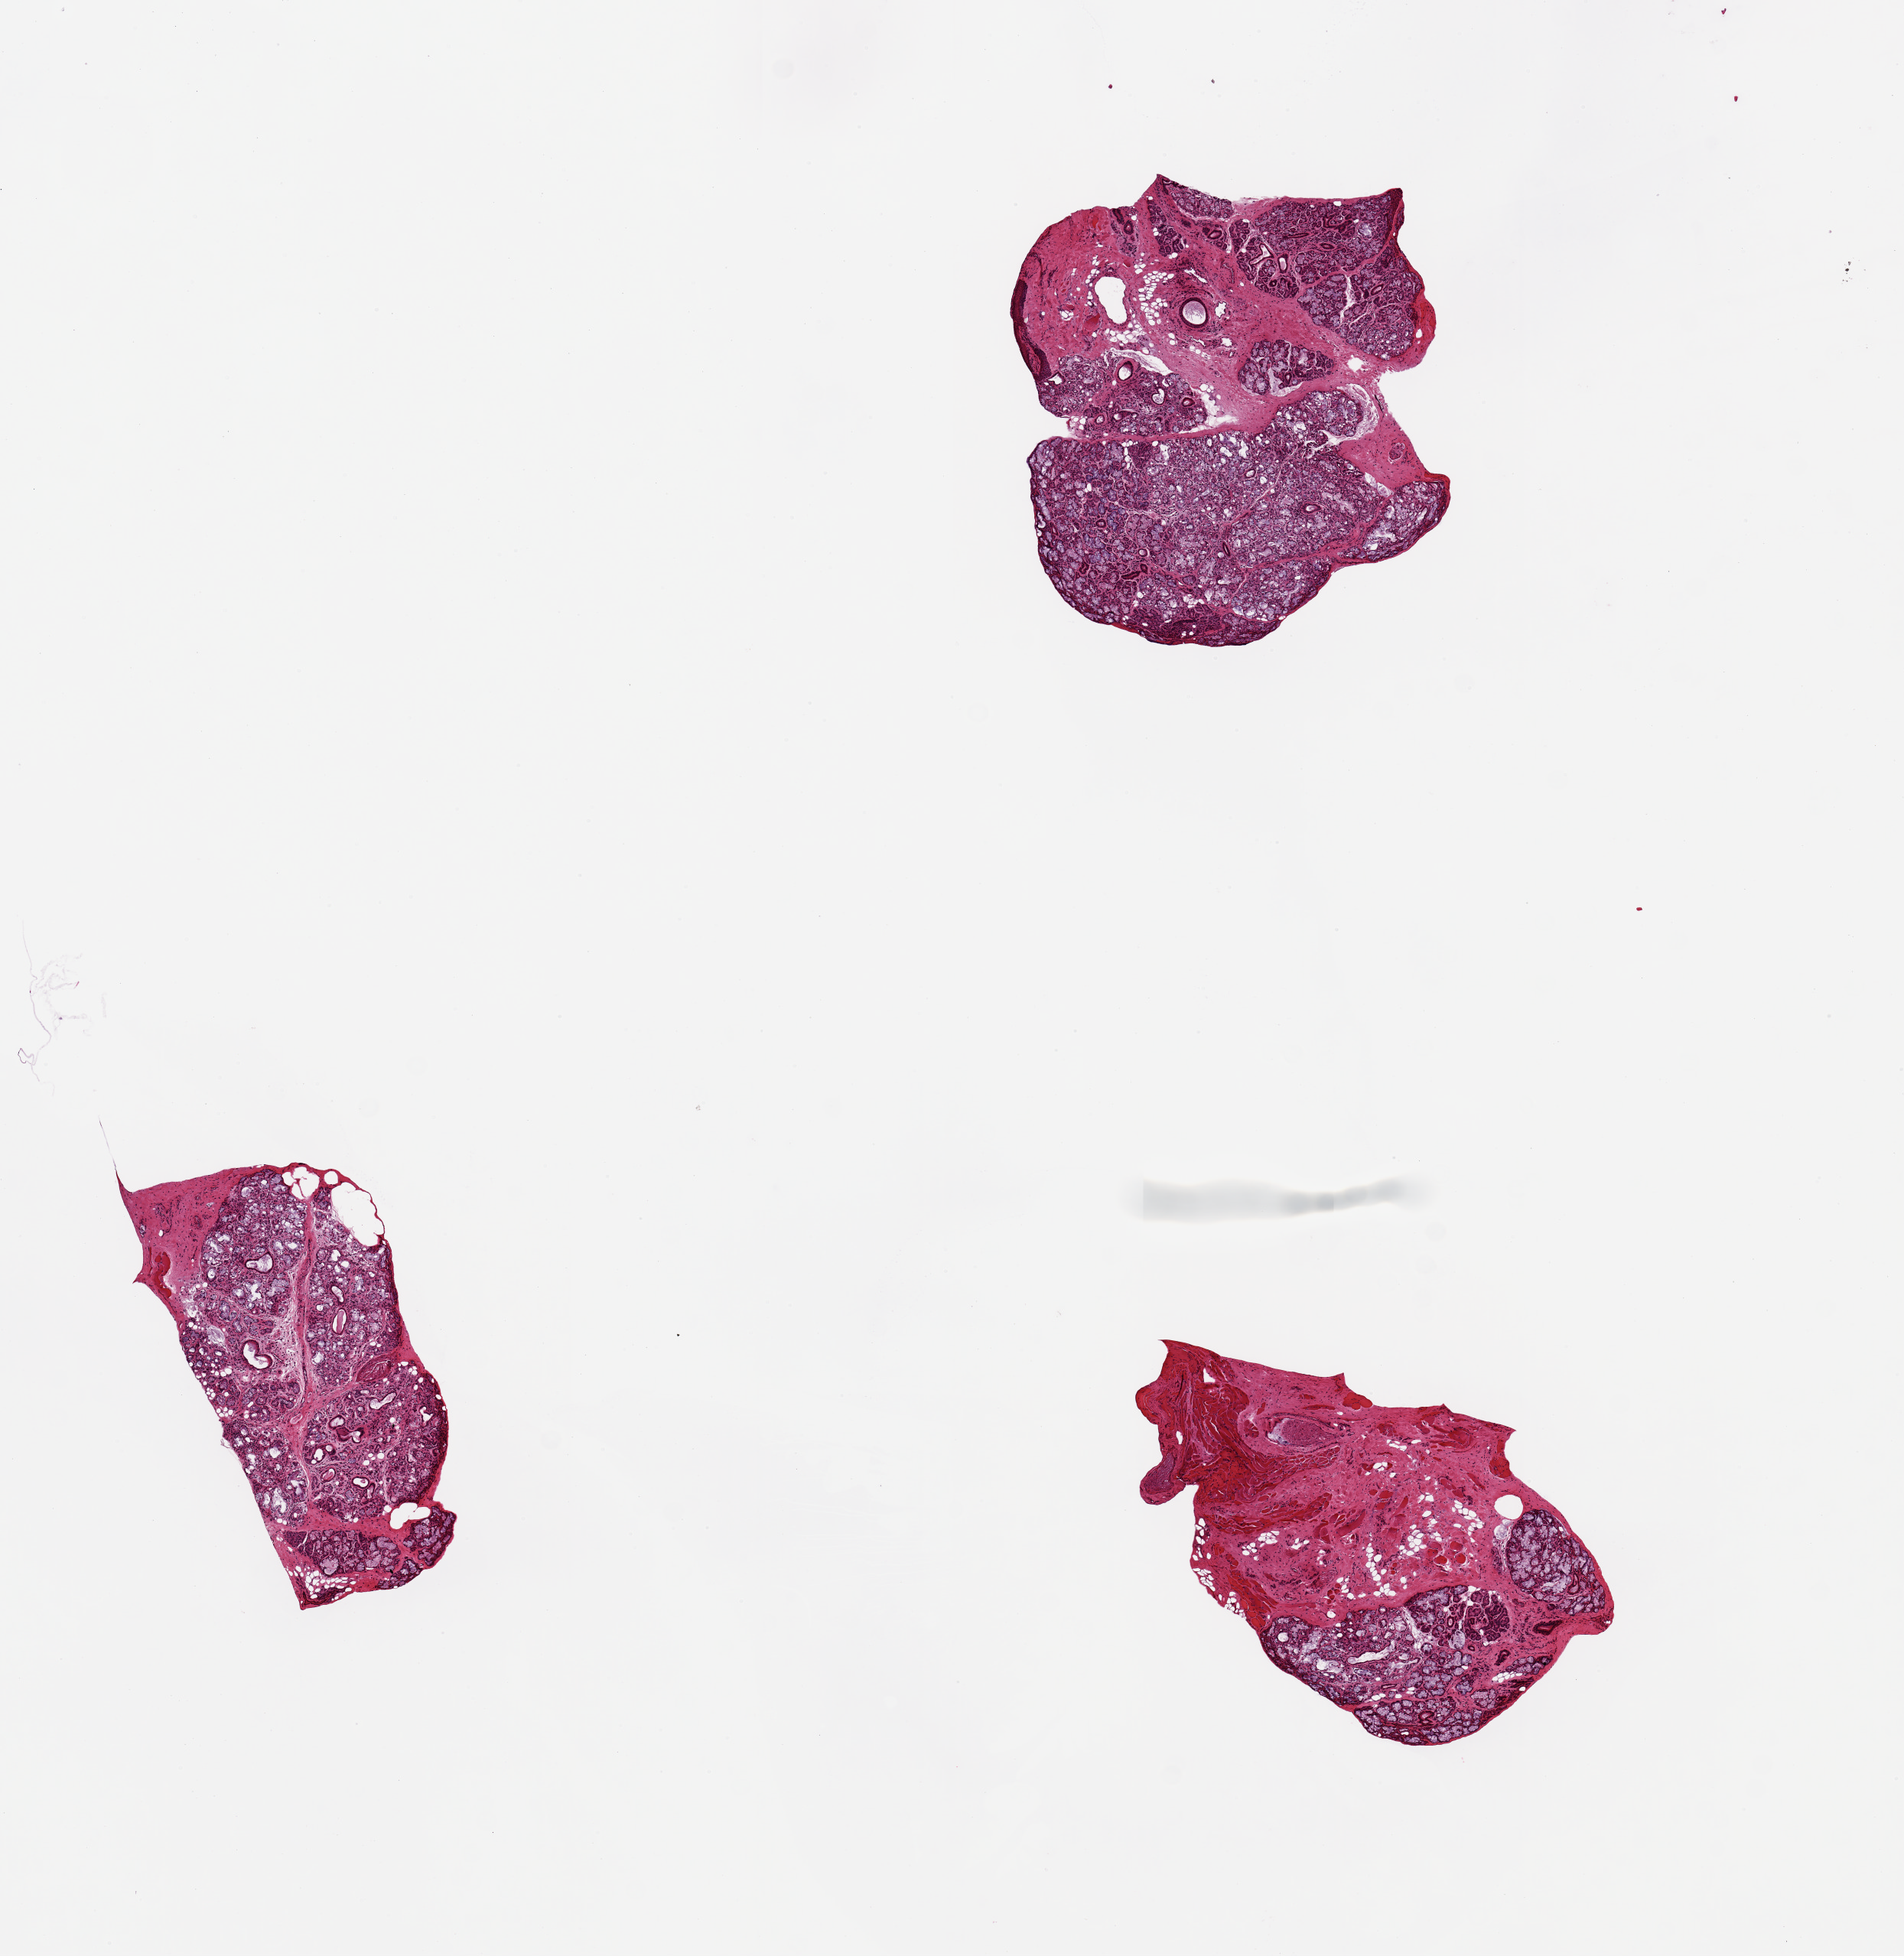
Haematoxylin and eosin whole-slide image, shown as a low-resolution overview of the whole scanned area (about 9.8 x 10.1 mm, from a 20x scan). PAXgene-fixed paraffin-embedded (PFPE) section. Sampled site (target tissue): minor salivary gland. Donor tissue sample.
• reviewer comment on this tissue sample: 3 pieces ~2.5mm, ranging from 30%-90% glandular tissue; rest is fibrovascular/muscular tissue